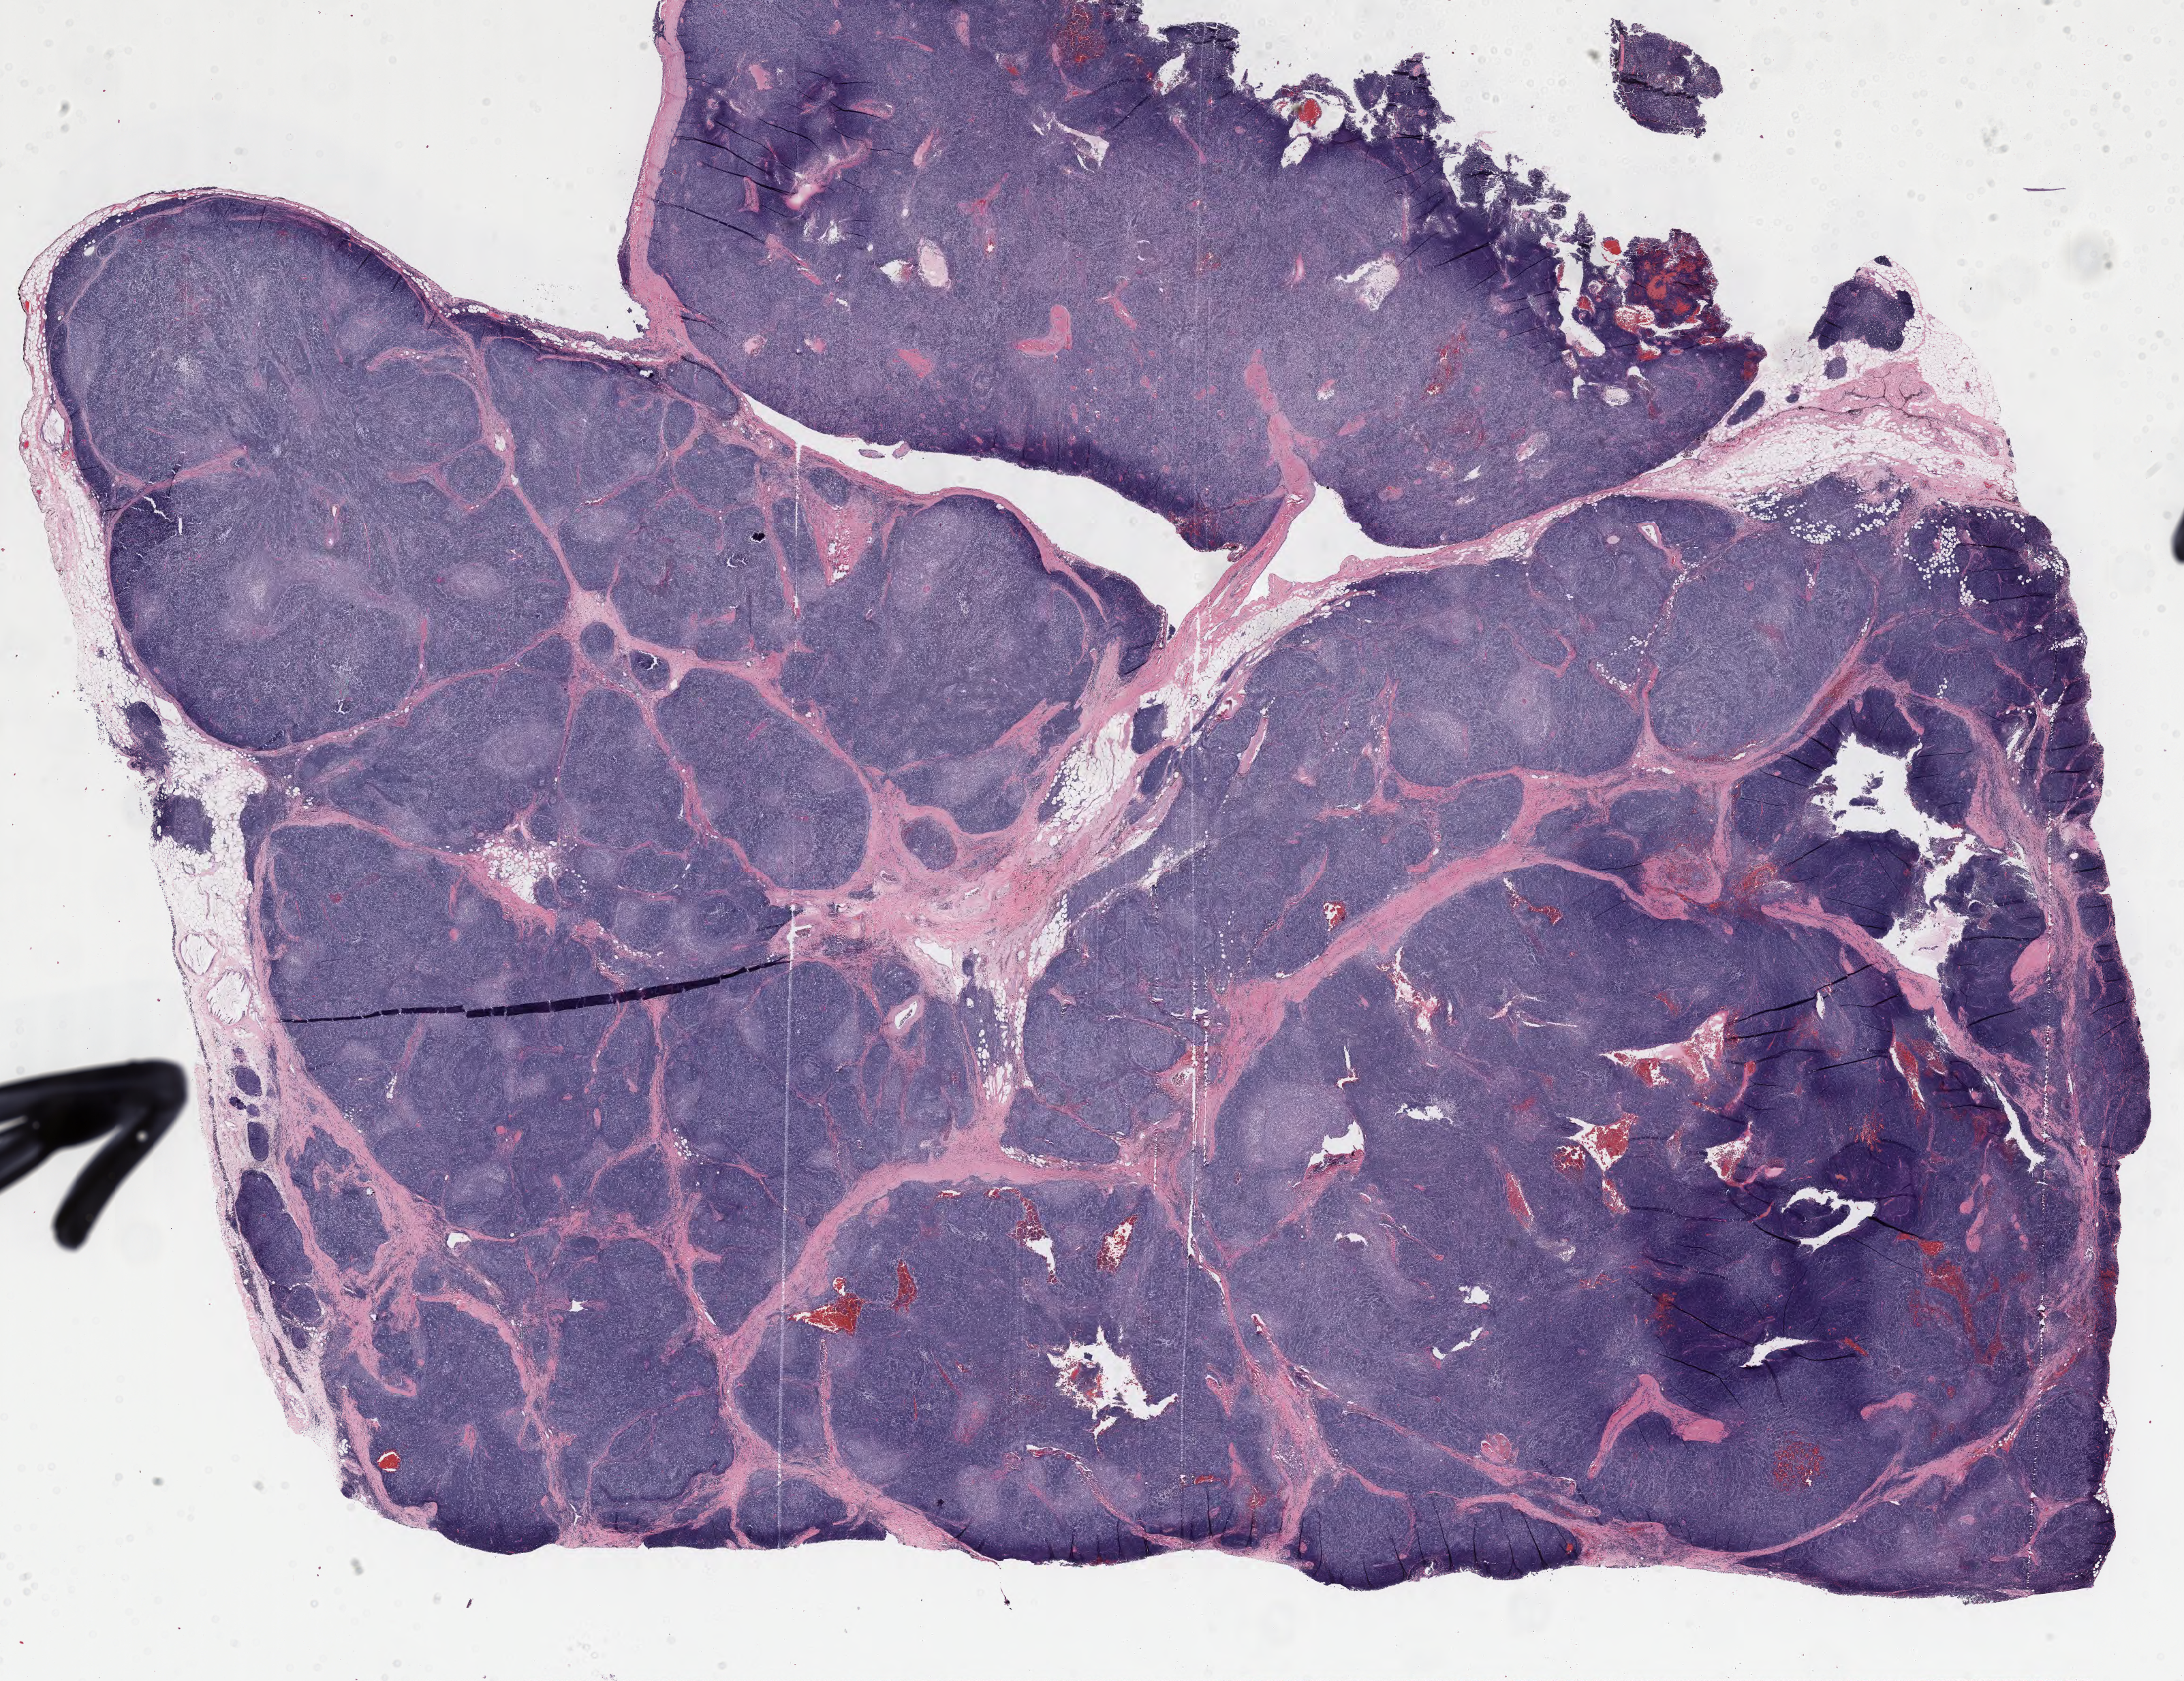
Digitized H&E tissue section (whole slide), low-resolution overview of the scanned area, about 25.4 x 19.6 mm, formalin-fixed paraffin-embedded (FFPE) diagnostic section, primary tumour sample from the thymus. Patient: male, age at initial diagnosis 44 years.
Pathologic diagnosis: Thymoma, type B2, malignant.